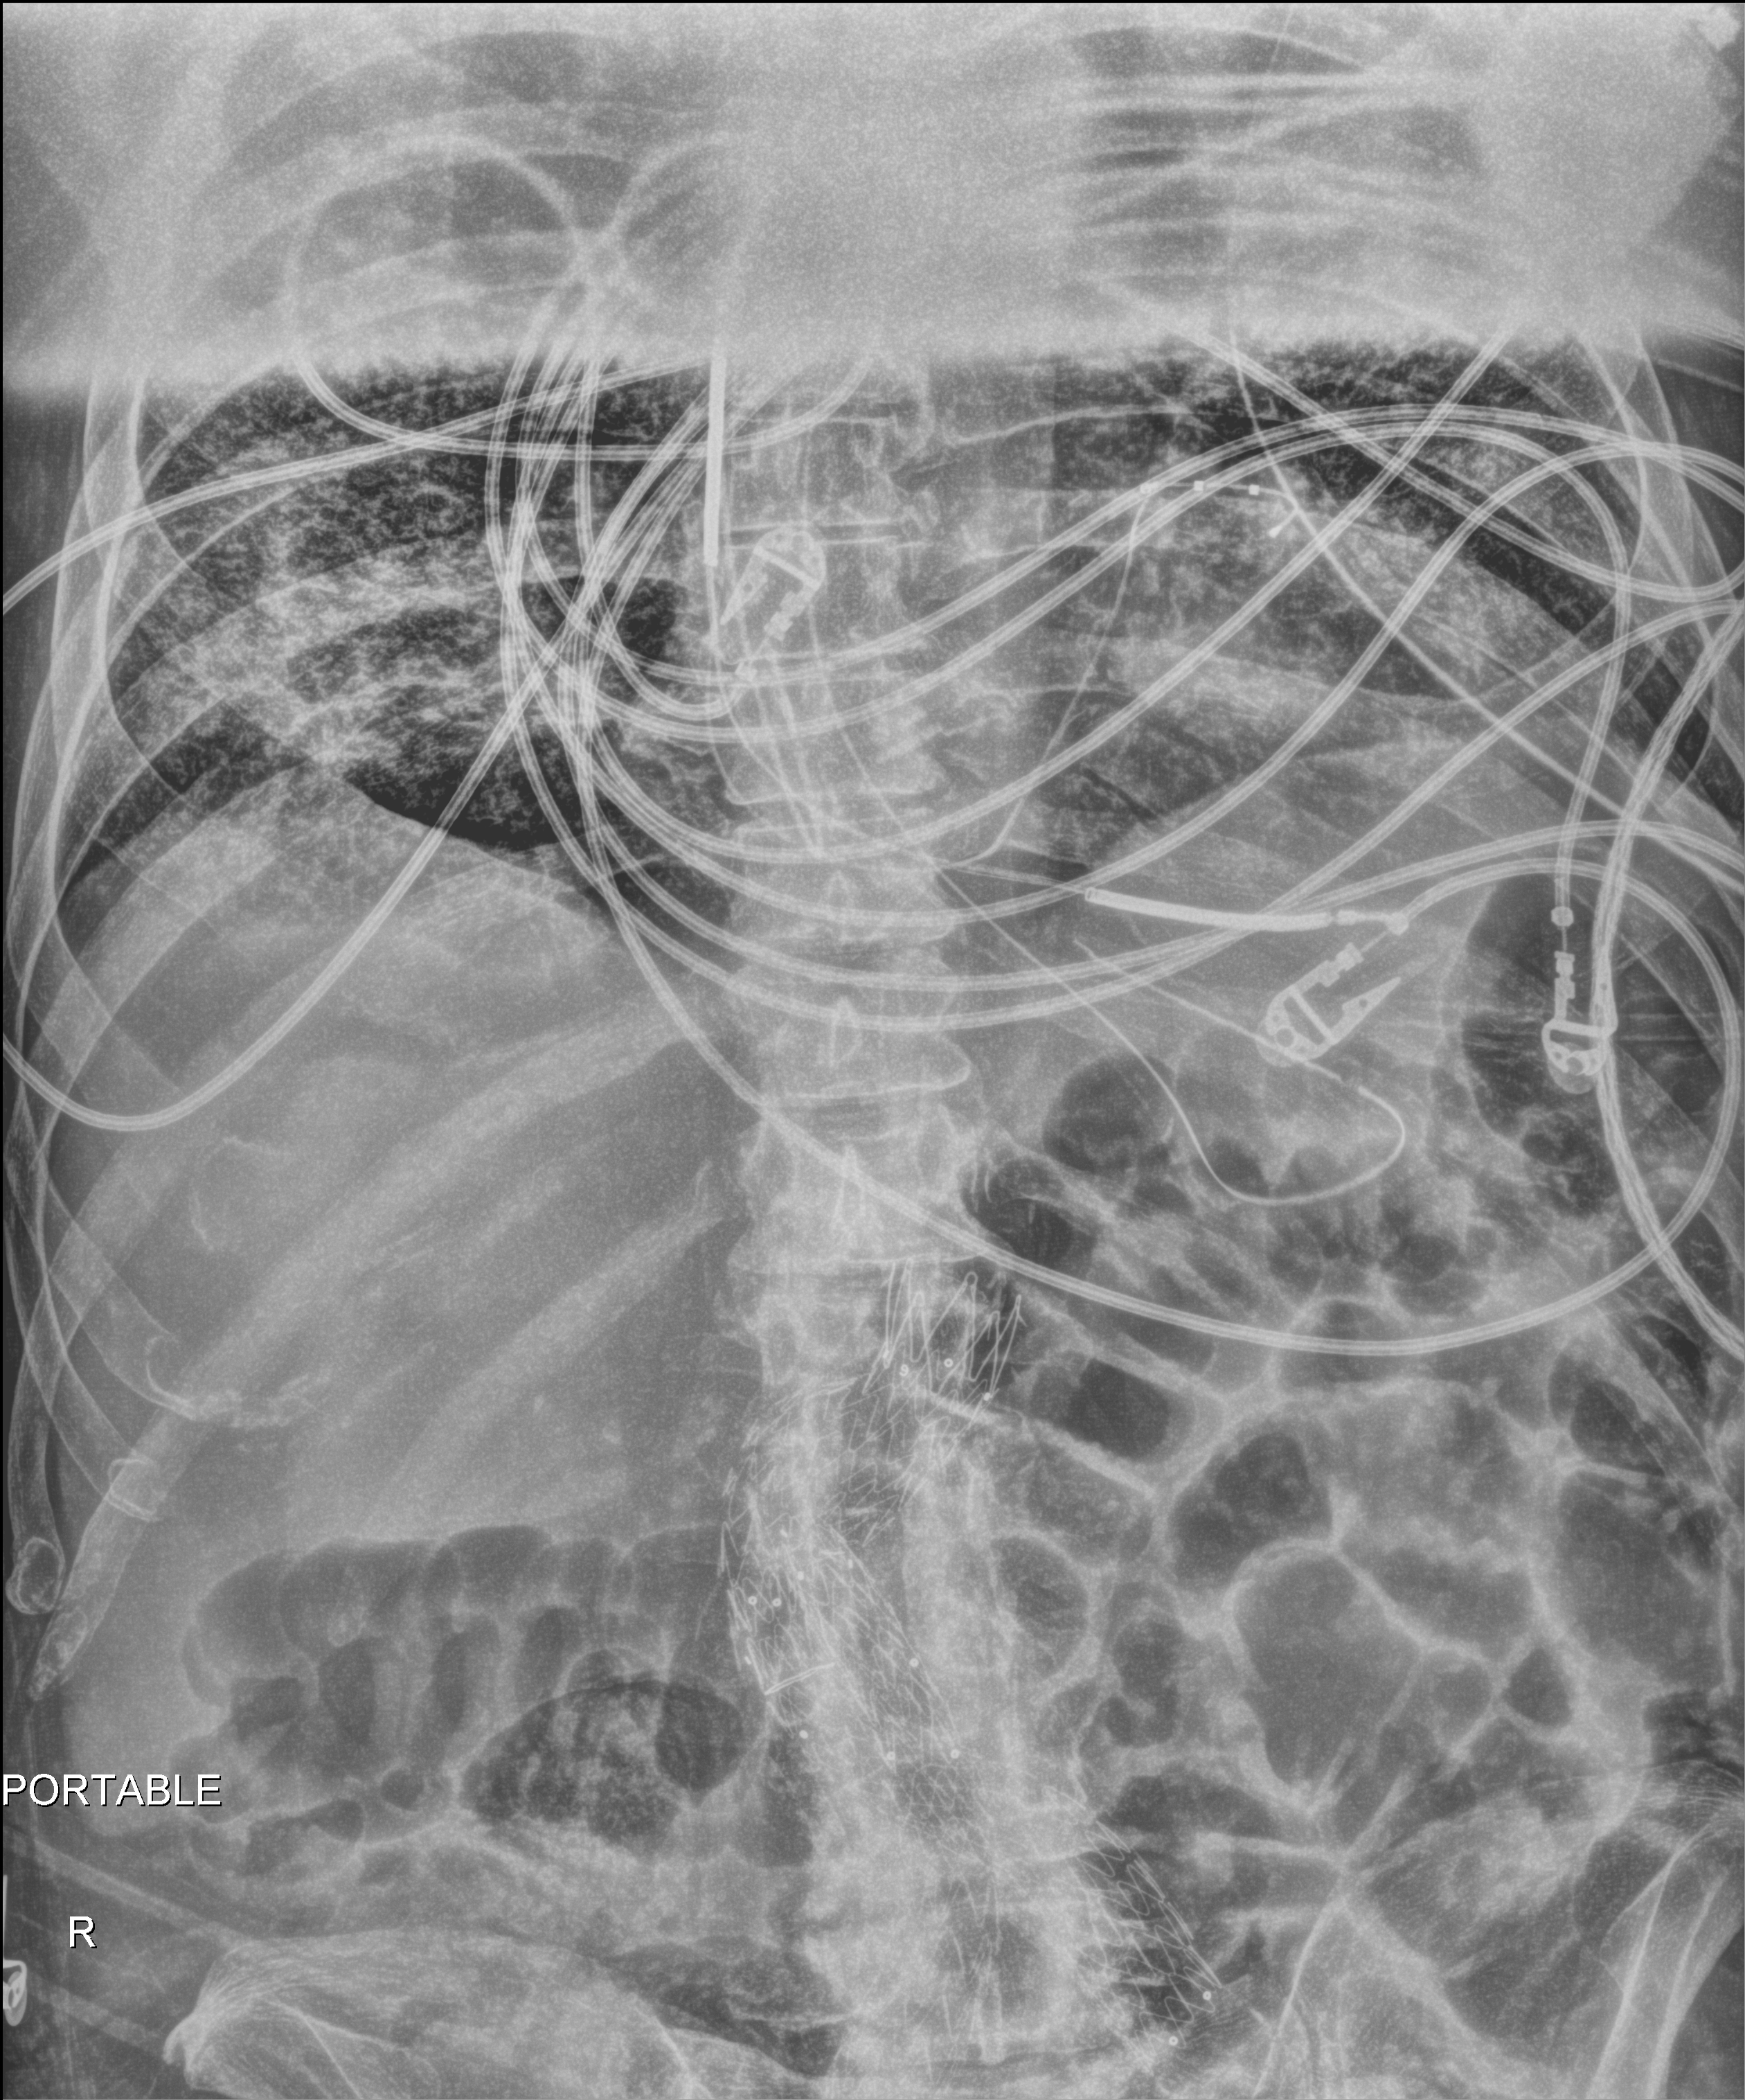
Abdomen X-ray (portable), anteroposterior (AP) projection. Male patient hospitalised with COVID-19, age 60–74 years.
Hospital-stay facts (about this admission, not read from this image; timing relative to this image not recorded):
- hypertension (admission record): yes
- mechanically ventilated during this hospital stay: yes
- chronic kidney disease (admission record): no